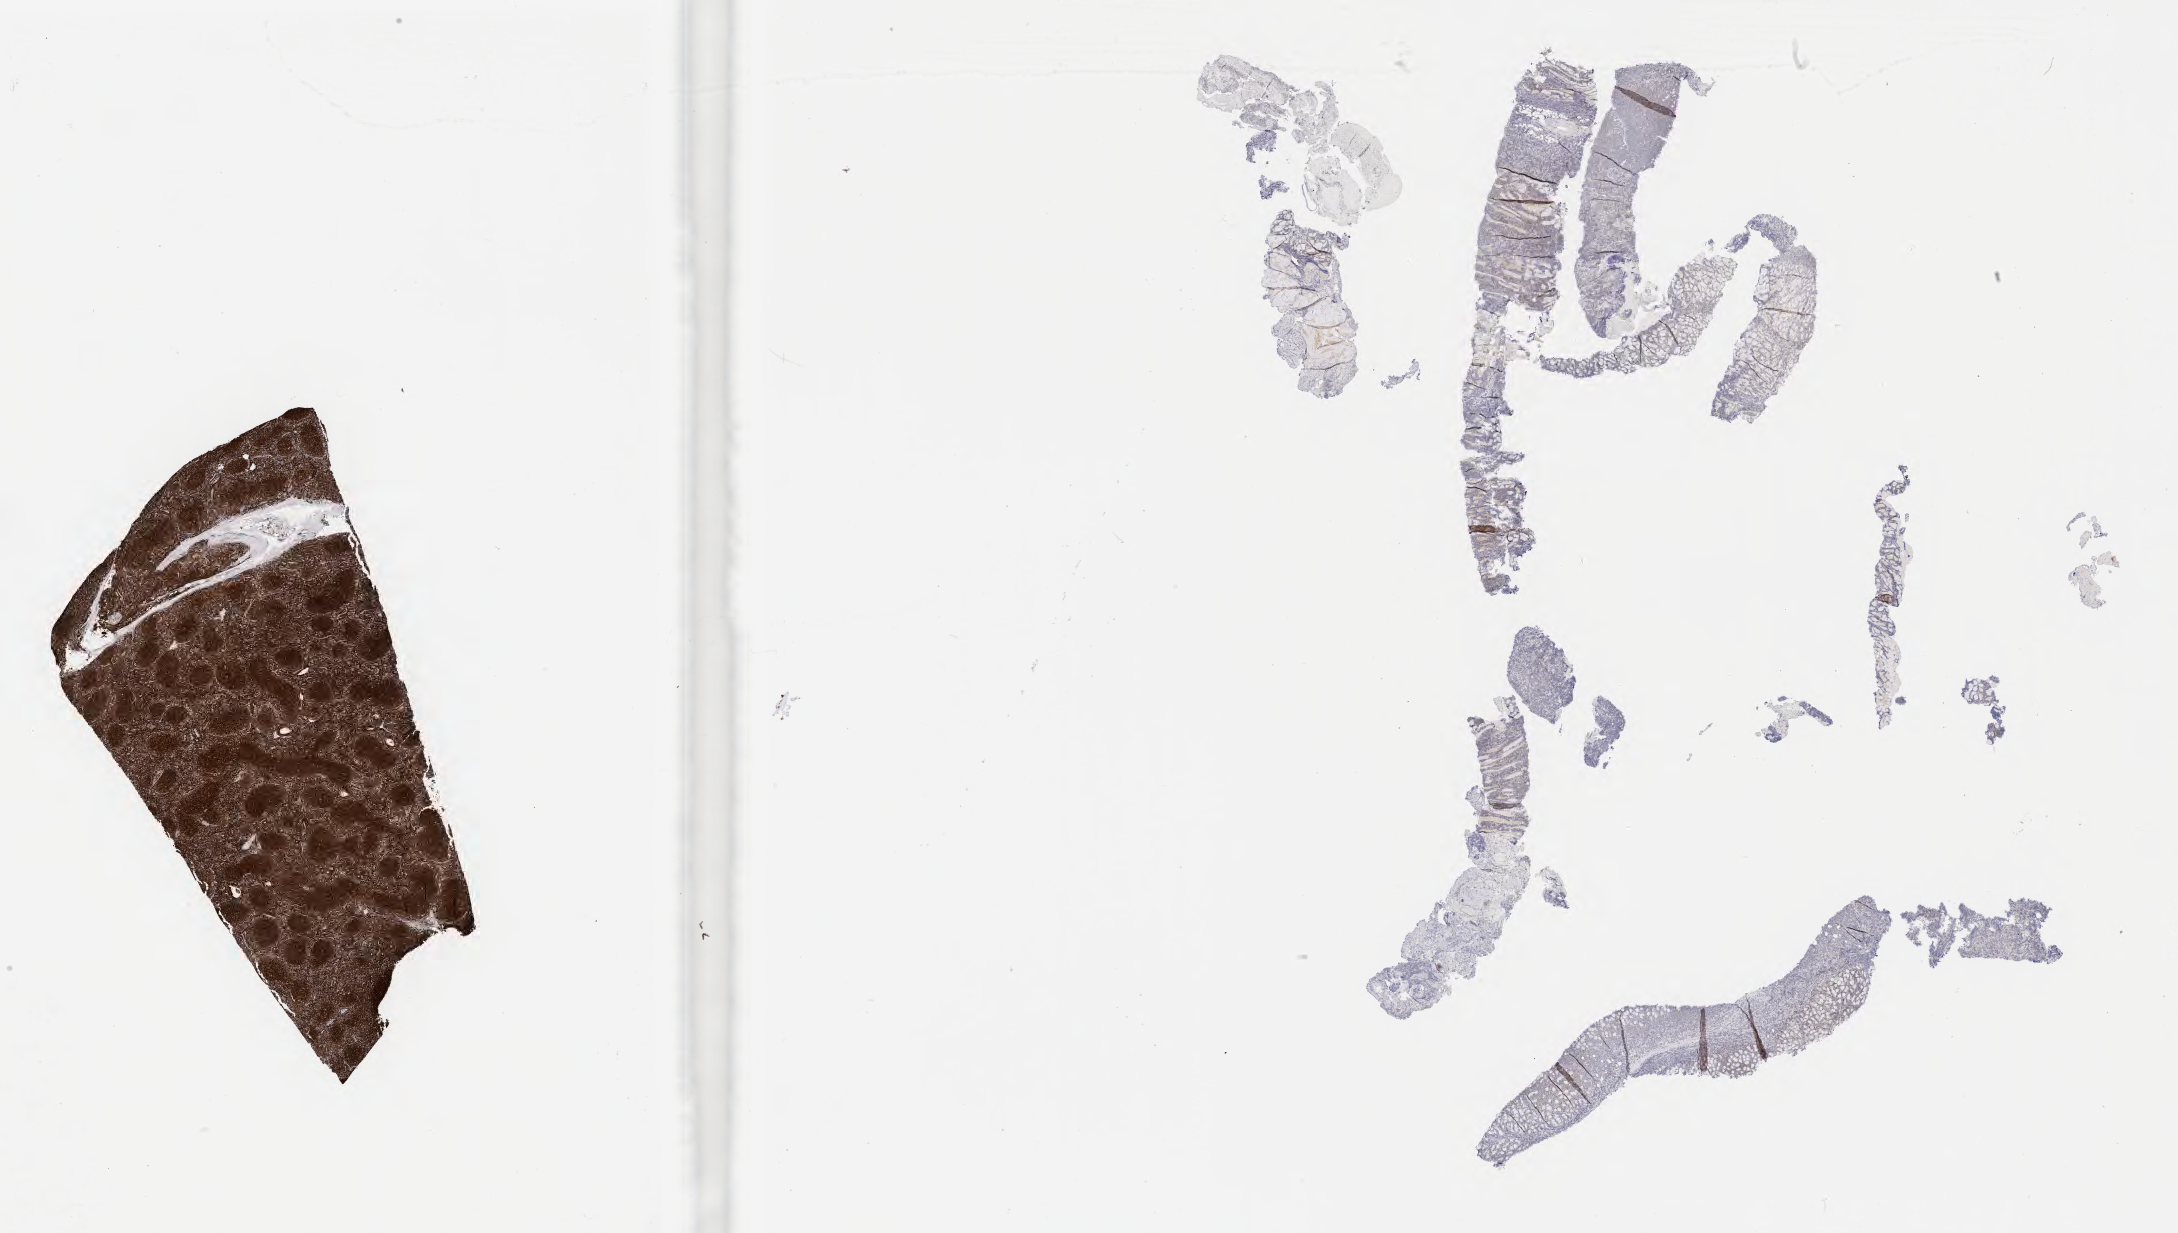
Whole-slide image, immunohistochemical stain for BCL2, whole scanned area (about 35.2 x 19.9 mm) shown as a low-resolution overview. Specimen: tumor tissue. Anatomic site: bone of pelvis. Male patient, aged 53.
Histologic diagnosis: Burkitt lymphoma, NOS.